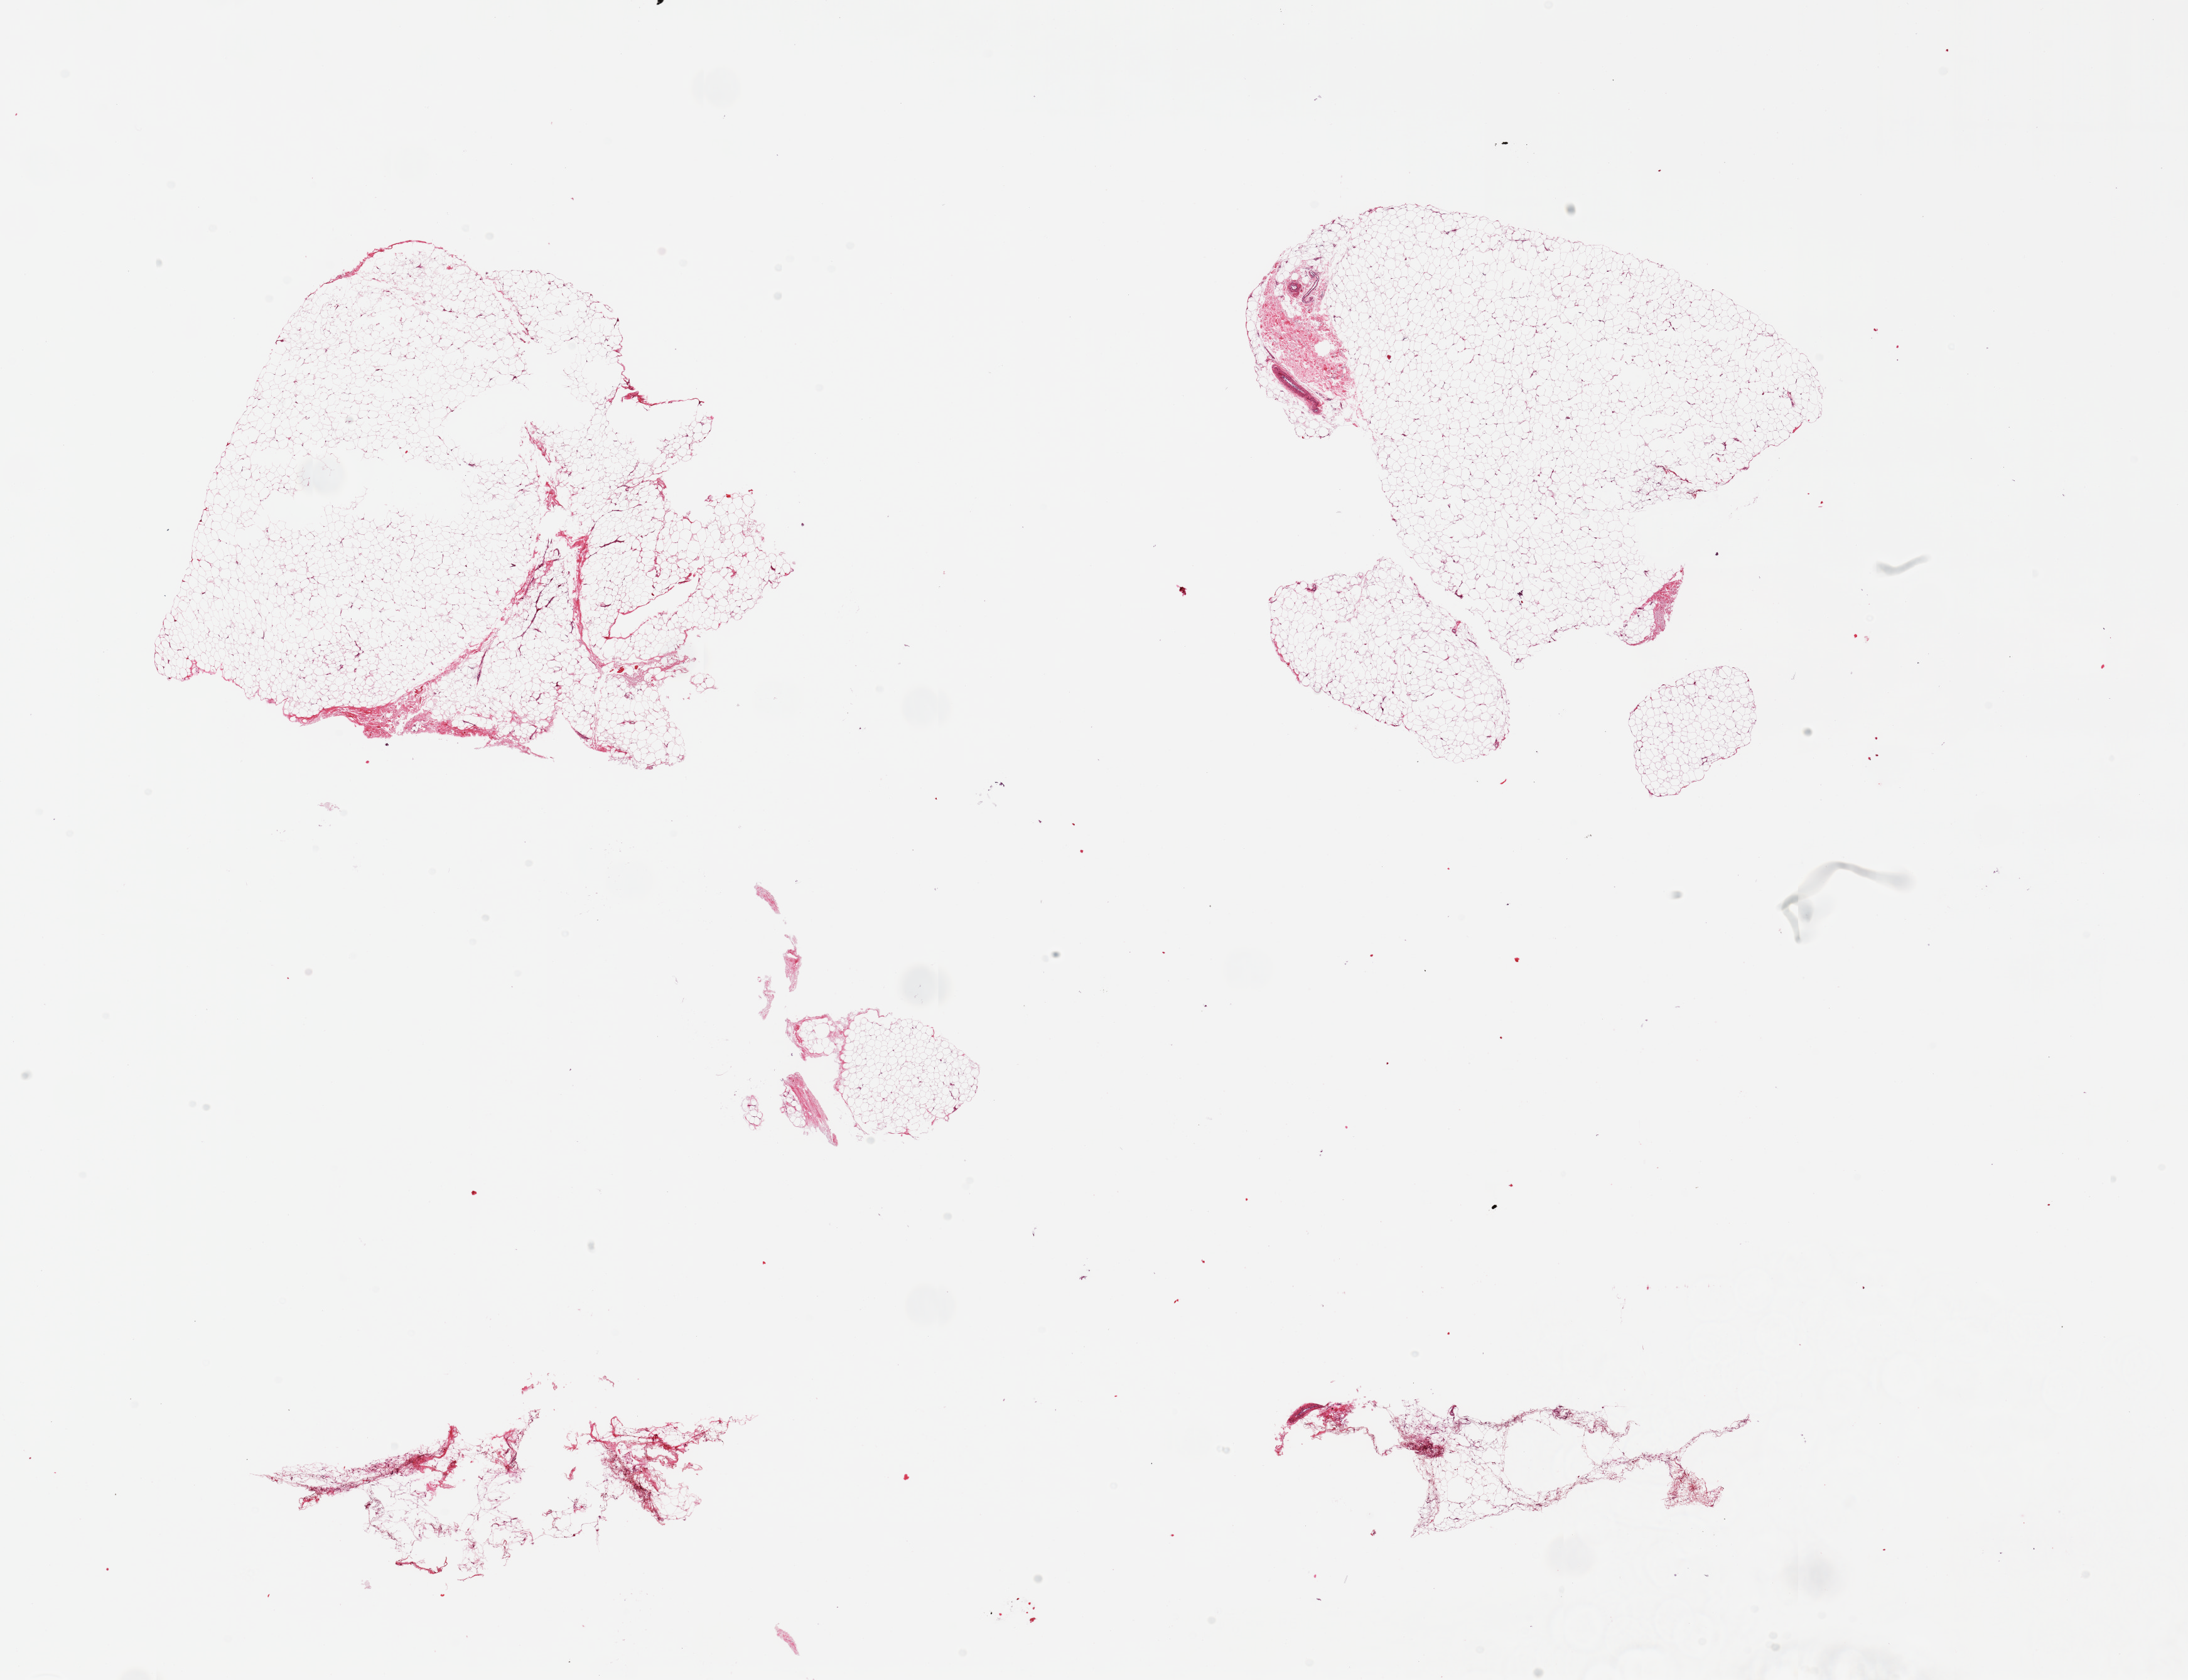
Hematoxylin and eosin (H&E) whole-slide image, whole scanned area (about 27.6 x 21.2 mm) shown as a low-resolution overview, PAXgene-fixed, paraffin-embedded tissue, sampled site (target tissue): adipose tissue, tissue donor sample. Donor: male.
Pathologist's review note for this sample: 2 pieces, < 5% fascia.